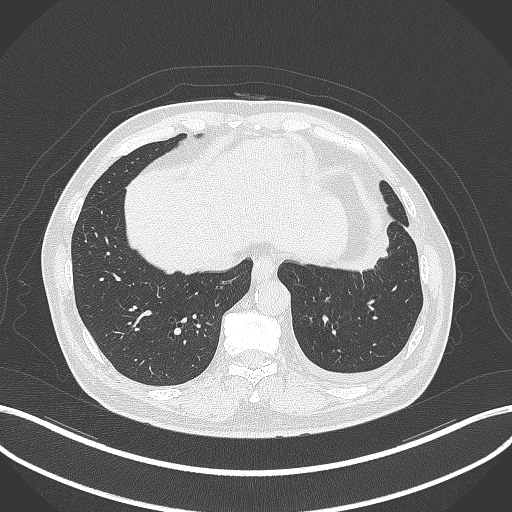
Chest CT, one axial slice; slice 84 of 230 in the series (ordered by position); reconstruction kernel B70f; lung window (W 1500 / L -600 HU); 1 mm slice thickness; 512 × 512 image matrix, field of view 400 × 400 mm. Patient: male, 68 years. Case-level facts recorded for this patient, not image findings: clinical TNM (as recorded): T2b N0 M0.
Outlined on this slice (rectangle marked by the reading radiologist):
- lung tumour (recorded histology: squamous cell carcinoma): bounding box (x1, y1, x2, y2) in pixels: (340, 228, 395, 281)